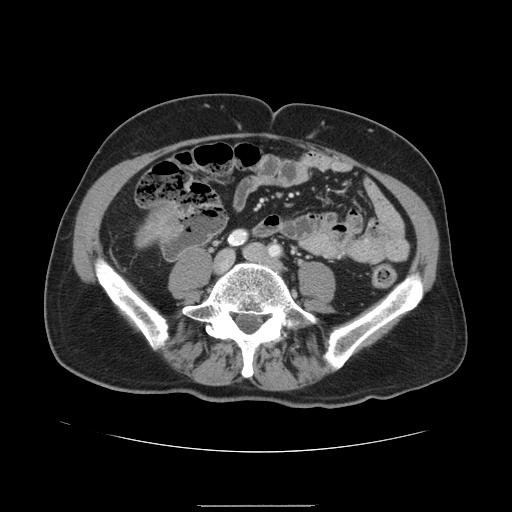
Contrast-enhanced abdominal CT, one axial slice. Slice 6 of 168 in the series (ordered by position). Intravenous contrast given. Soft-tissue window (W 400 / L 40 HU). 512 × 512 image matrix. Male patient, age 74 years. Case-level facts recorded for this patient, not image findings: diagnosis: colorectal cancer liver metastases, imaged before liver resection.
Structures marked on this image (outlined manually by an expert reader):
- liver: box from (x=137, y=201) to (x=186, y=246) px
- liver metastasis: (x=140, y=209)–(x=179, y=240)